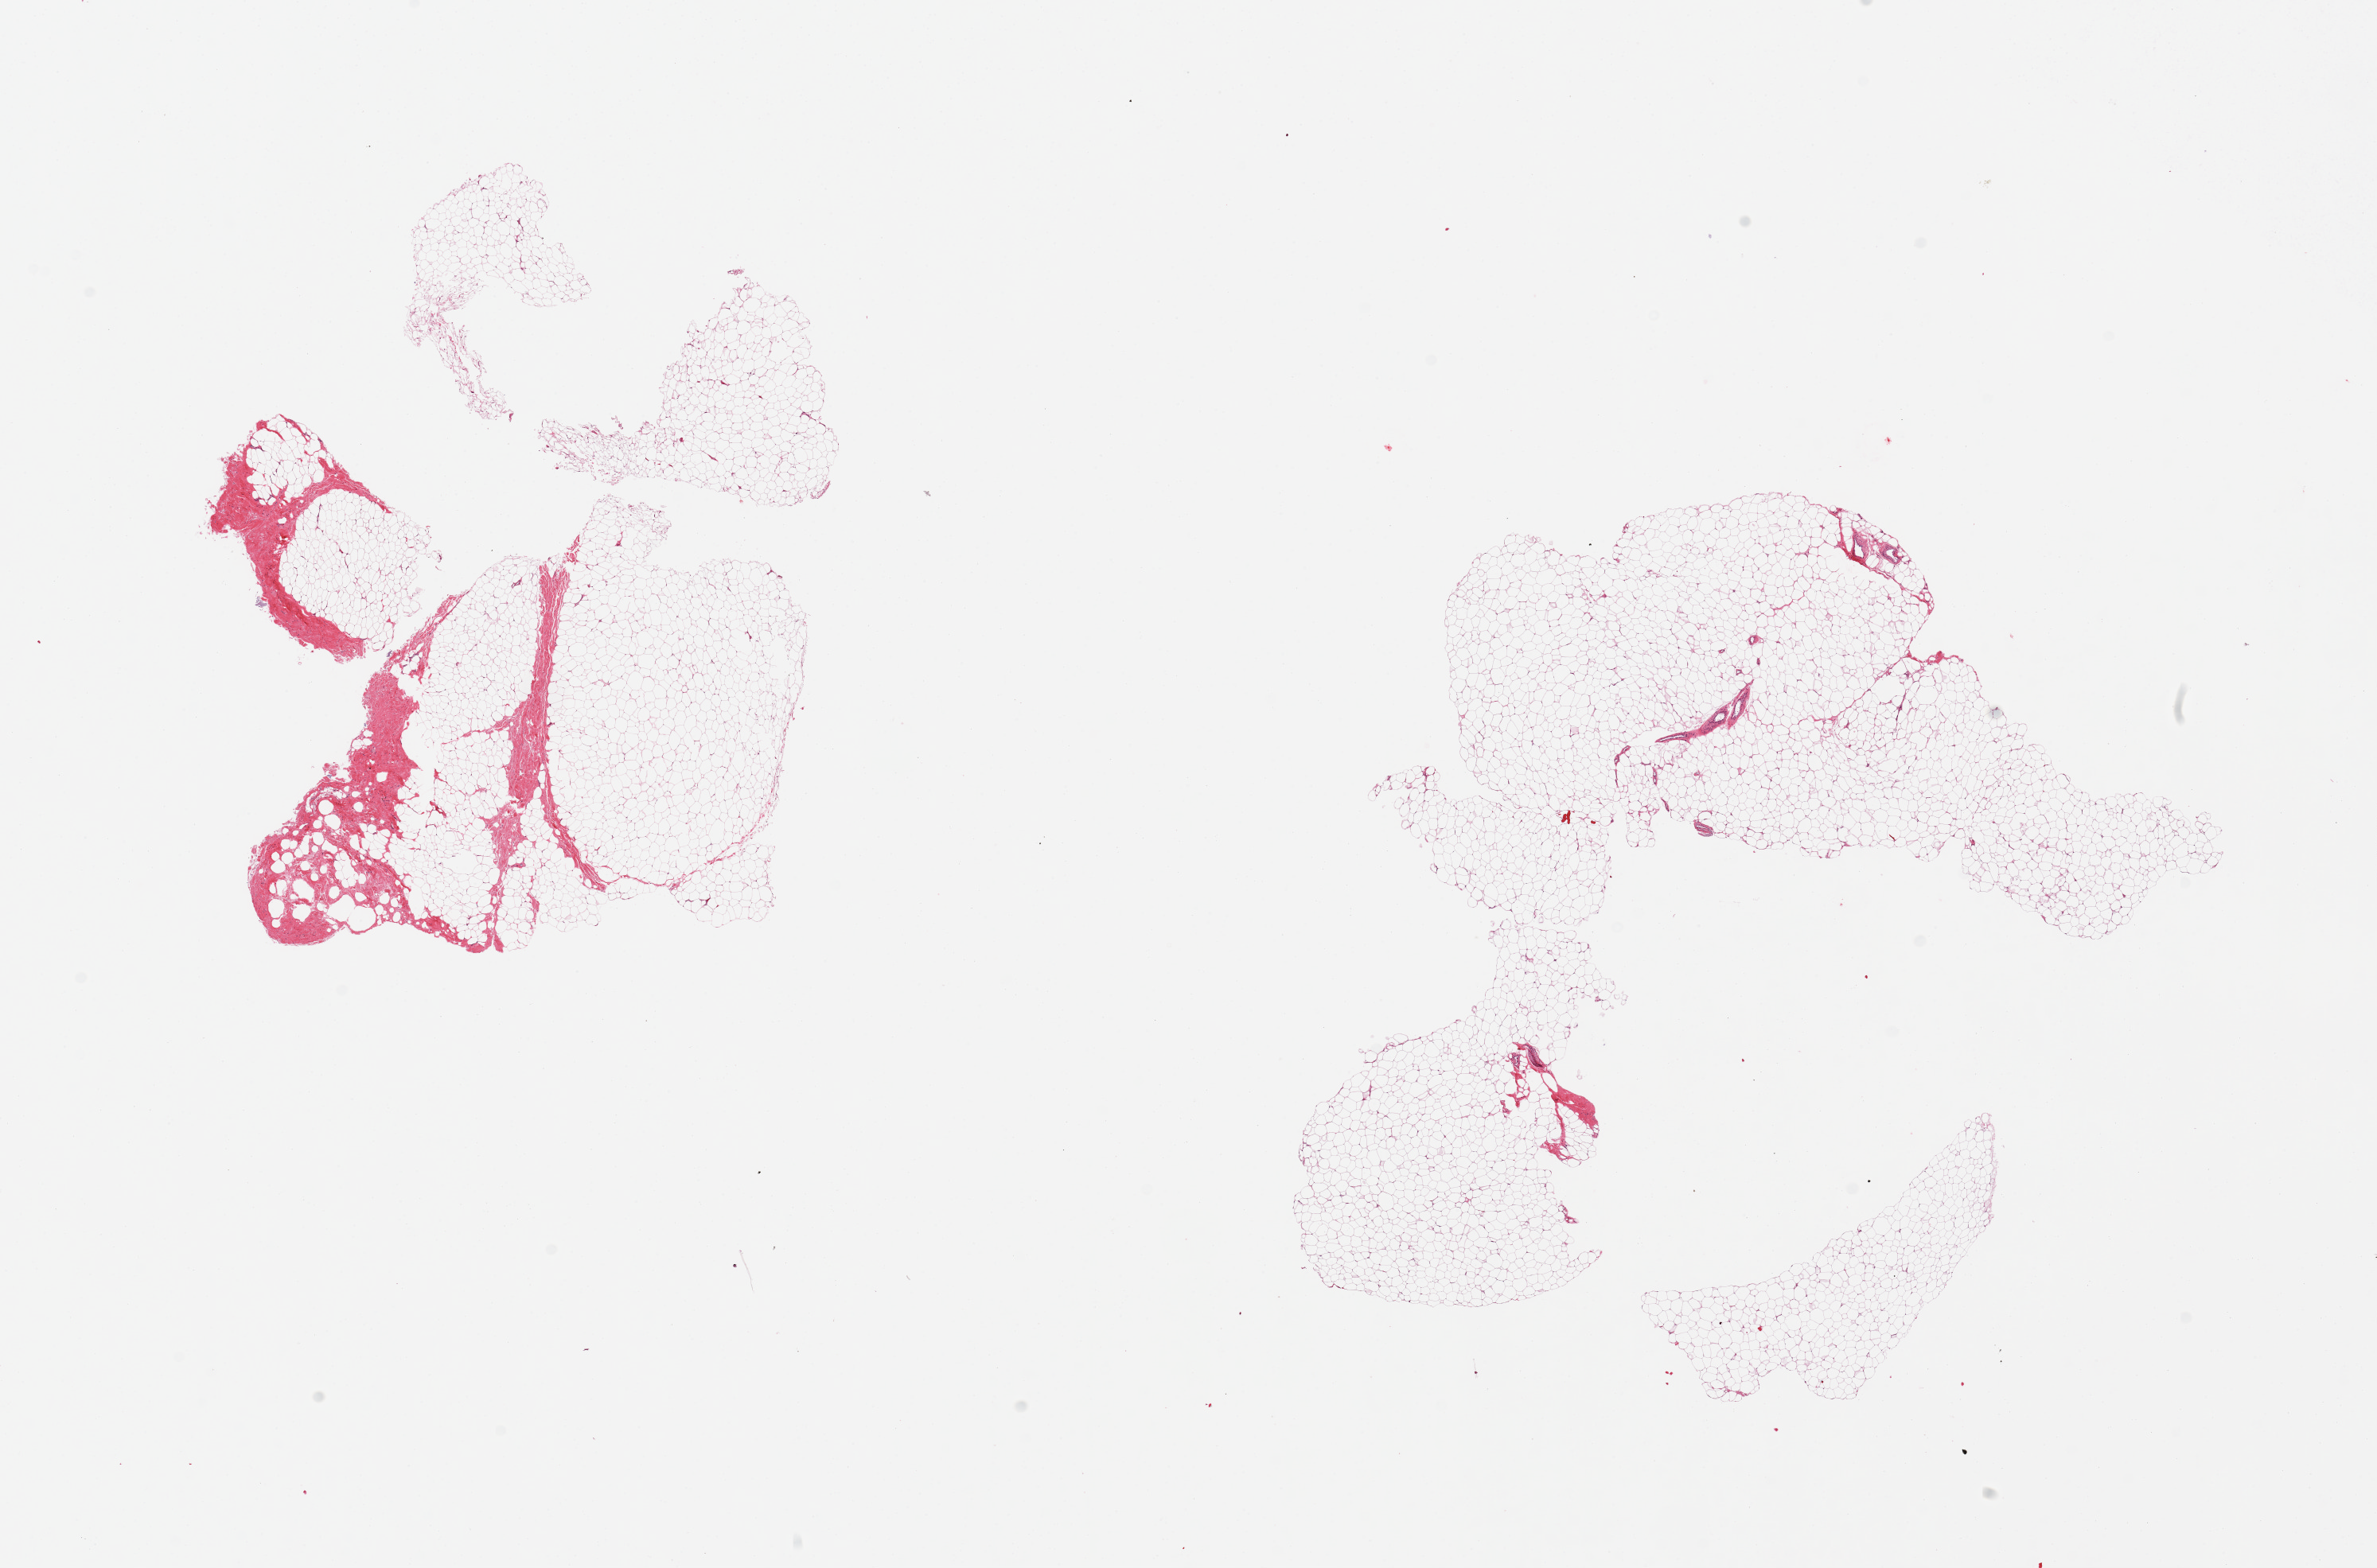
Whole-slide image, H&E stain, a low-resolution overview of the entire scanned area, about 23.6 x 15.6 mm; PAXgene-fixed paraffin-embedded (PFPE) section; target tissue: breast; donor tissue sample. Donor sex: male.
Pathologist's review note for this sample: 2 pieces; fat, up to 10% fibrous stroma in one piece.